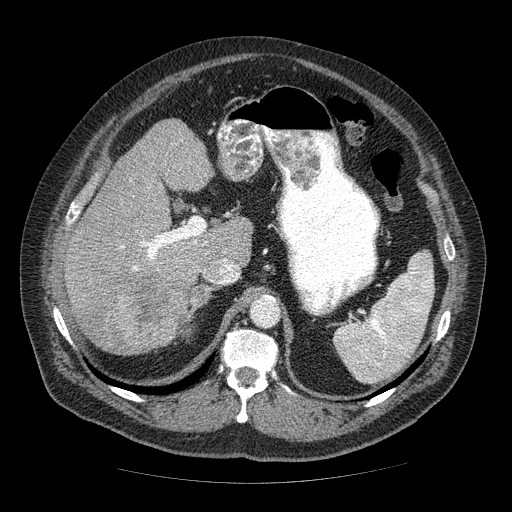
Contrast-enhanced abdominal CT (liver protocol), one axial slice; position 36 of 85 along the scan axis; soft-tissue window (W 400 / L 40 HU); 2.5 mm slice thickness; 512 × 512 image matrix, field of view 420 × 420 mm. Case-level facts recorded for this patient, not image findings: diagnosis: hepatocellular carcinoma (patient treated with transarterial chemoembolisation; whether this scan precedes or follows treatment is not stated here); TNM stage (as recorded): Stage-IIIA; Child-Pugh class: A; tumour nodularity: multinodular; tumour size: 7 cm.
Structures marked on this image (semi-automatically segmented with operator editing):
- liver parenchyma outside the tumour (the mass and vessels are separate outlines, so this box may not span the whole liver): bounding box <64,120,252,352> (left, top, right, bottom; pixels)
- mass: <74,269,193,356>
- liver vessels: <120,232,239,271>